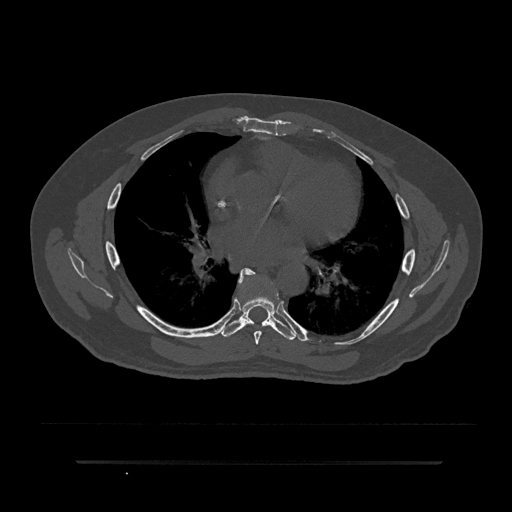
CT including the spine, one axial slice. Slice 499 of 797 in the series (ordered by position). Reconstruction kernel Br40s/3. Bone window (W 1800 / L 400 HU). 0.5 mm slice thickness. 512 × 512 image matrix, field of view 464 × 464 mm. Male patient, age 59 years. From the clinical record (not read from this slice): primary cancer: bile ducts.
Annotated regions visible in this slice (semi-automatically segmented with operator editing):
- T6 vertebra: bounding box (x1, y1, x2, y2) in pixels: (238, 268, 268, 345)
- T7 vertebra: (221, 268, 296, 340)